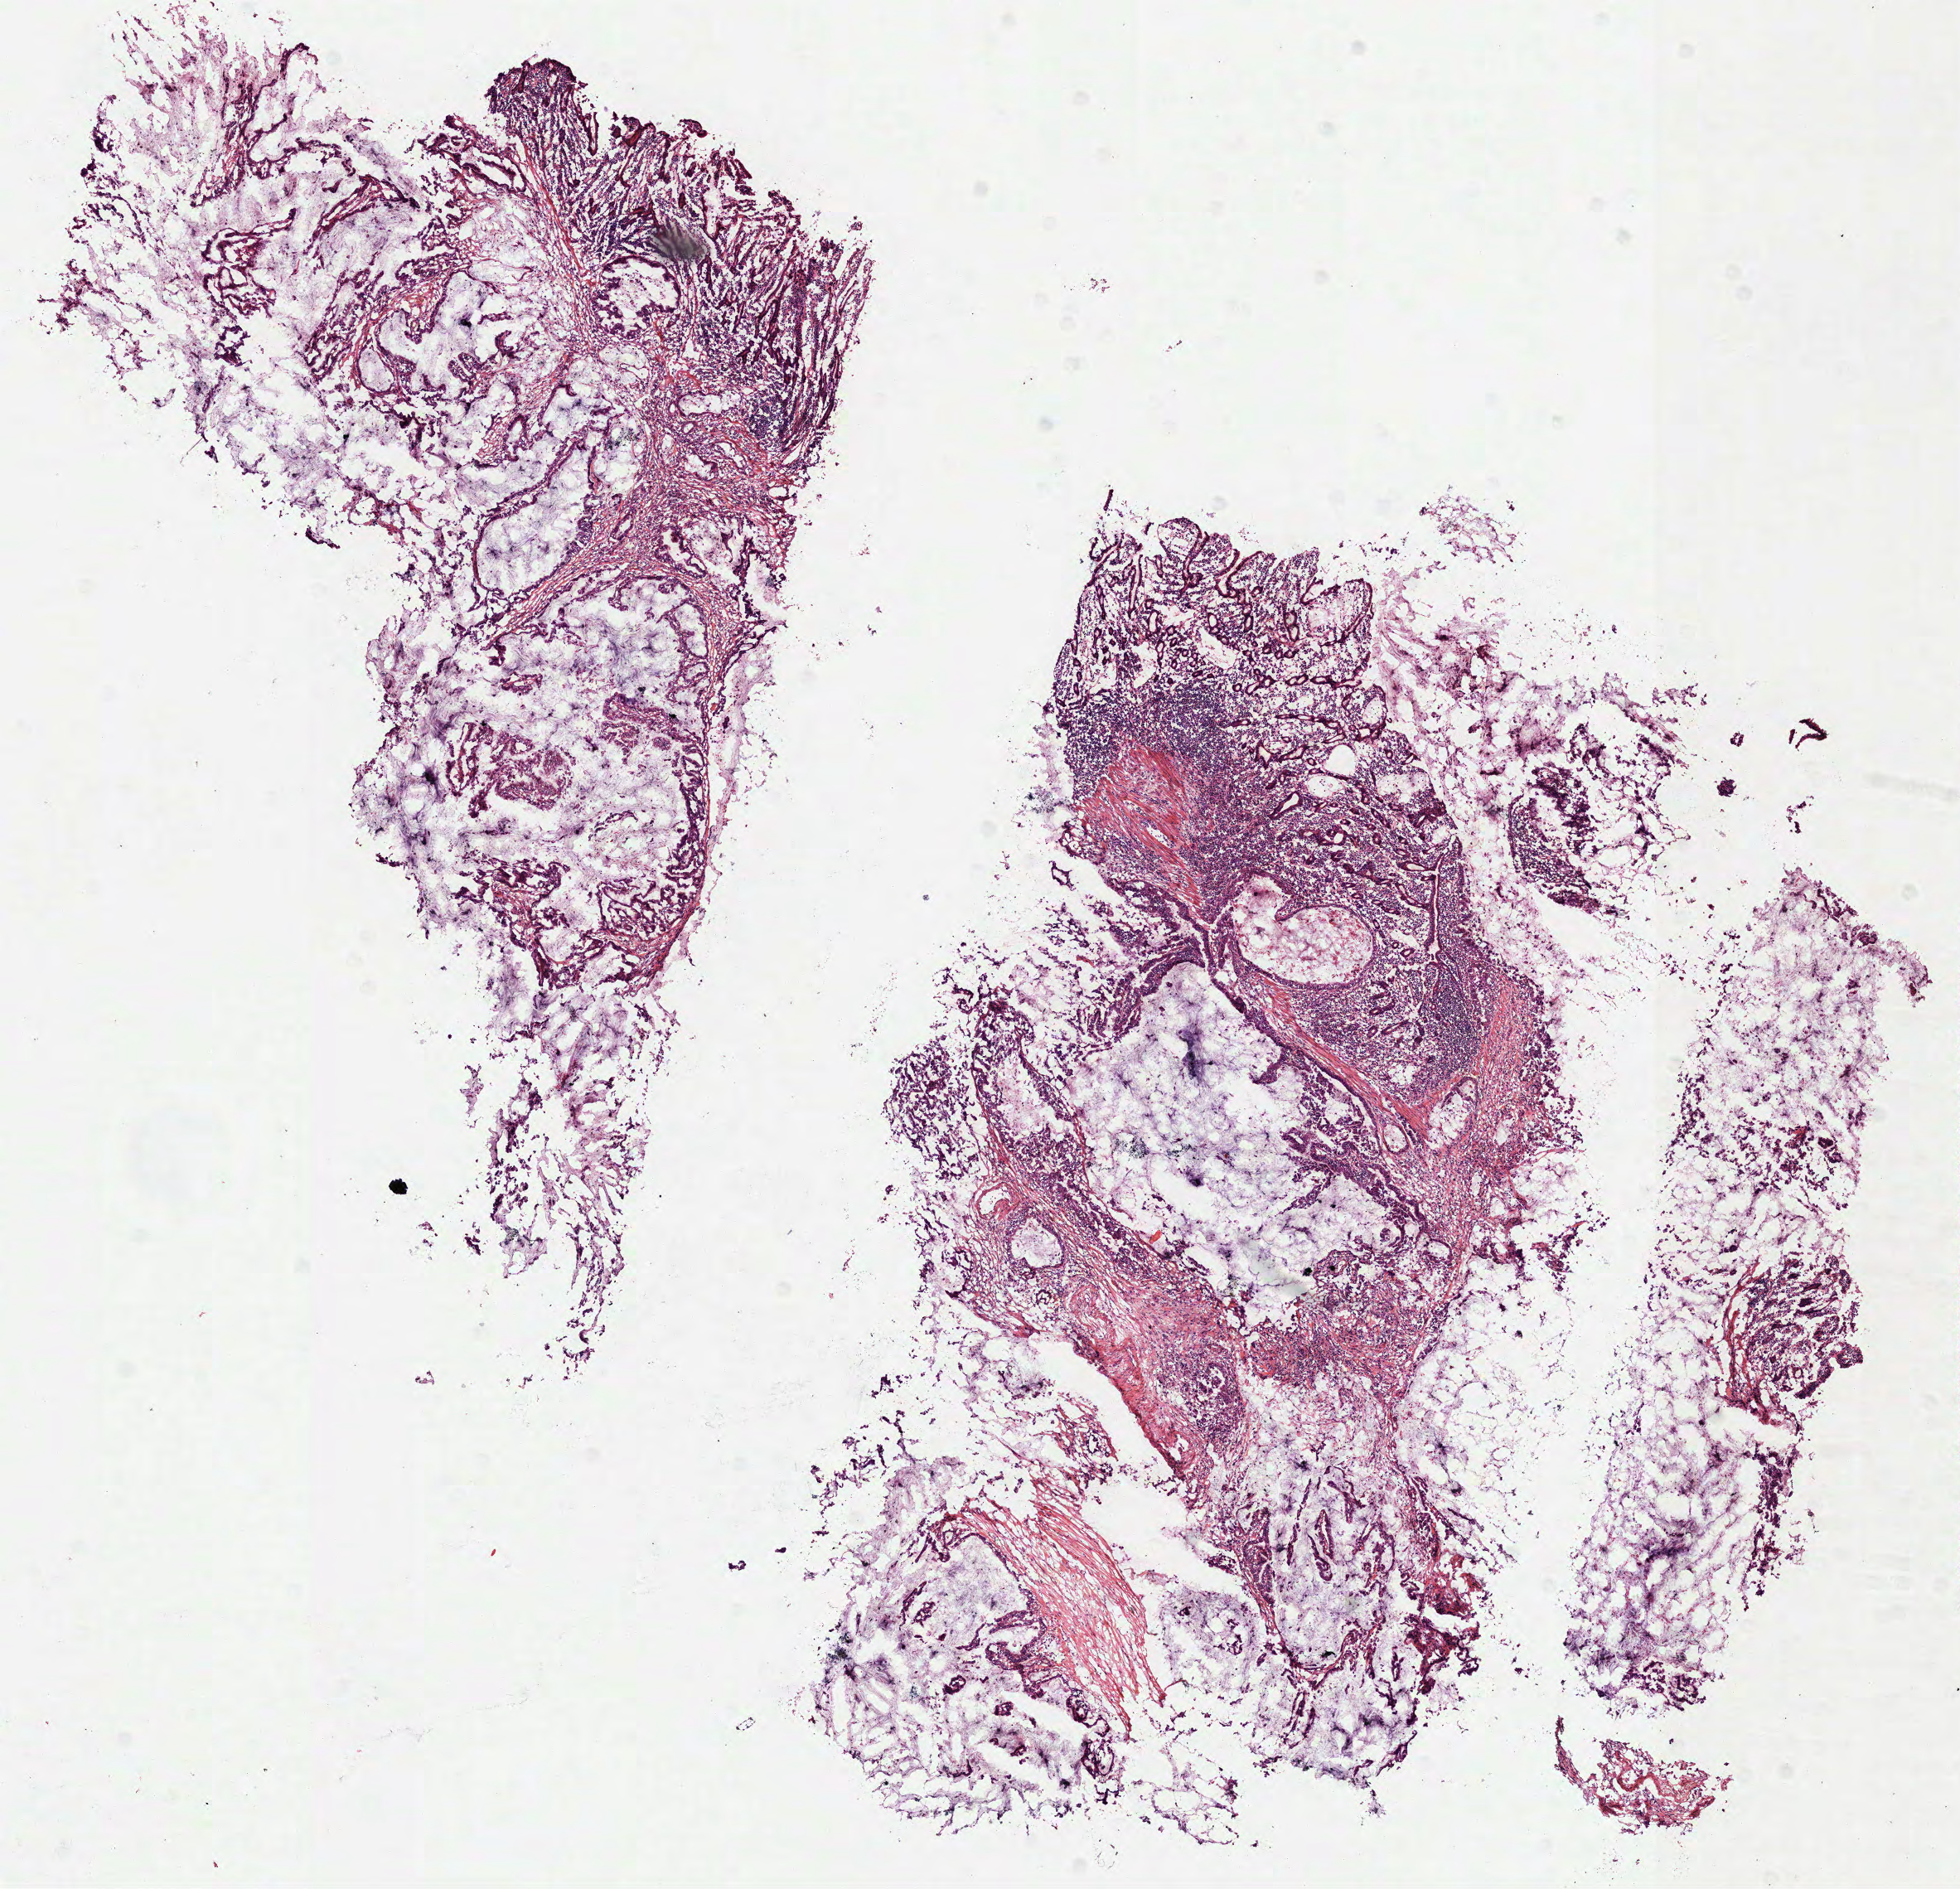
Whole-slide histology image, Hematoxylin and eosin (H&E) stained — a low-resolution overview of the entire scanned area, about 9.5 x 9.2 mm; frozen section from the top of the tissue portion; stomach, primary tumour sample. Patient: male, age at initial diagnosis 65 years. Histologic grade: G2 (moderately differentiated). Composition of this section per pathologist review: tumour cells 80%, tumour nuclei 70%, normal cells 10%, stromal cells 10%, necrosis 0%.
- histologic diagnosis: Mucinous adenocarcinoma (gastric antrum)
- AJCC pathologic stage: IV (6th edition)